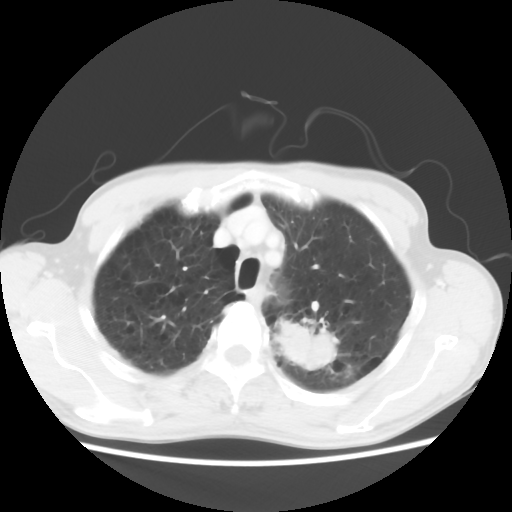
Chest CT, one axial slice. Position 51 of 64 along the scan axis. 120 kVp. Lung window (W 1500 / L -600 HU). 5 mm slice thickness. 512 × 512 image matrix. Male patient, age 63 years. Case-level facts recorded for this patient, not image findings: clinical TNM (as recorded): T2 N0 M0.
Structures marked on this image (bounding box drawn by a radiologist):
- lung tumour (recorded histology: adenocarcinoma): box from (x=276, y=314) to (x=341, y=380) px